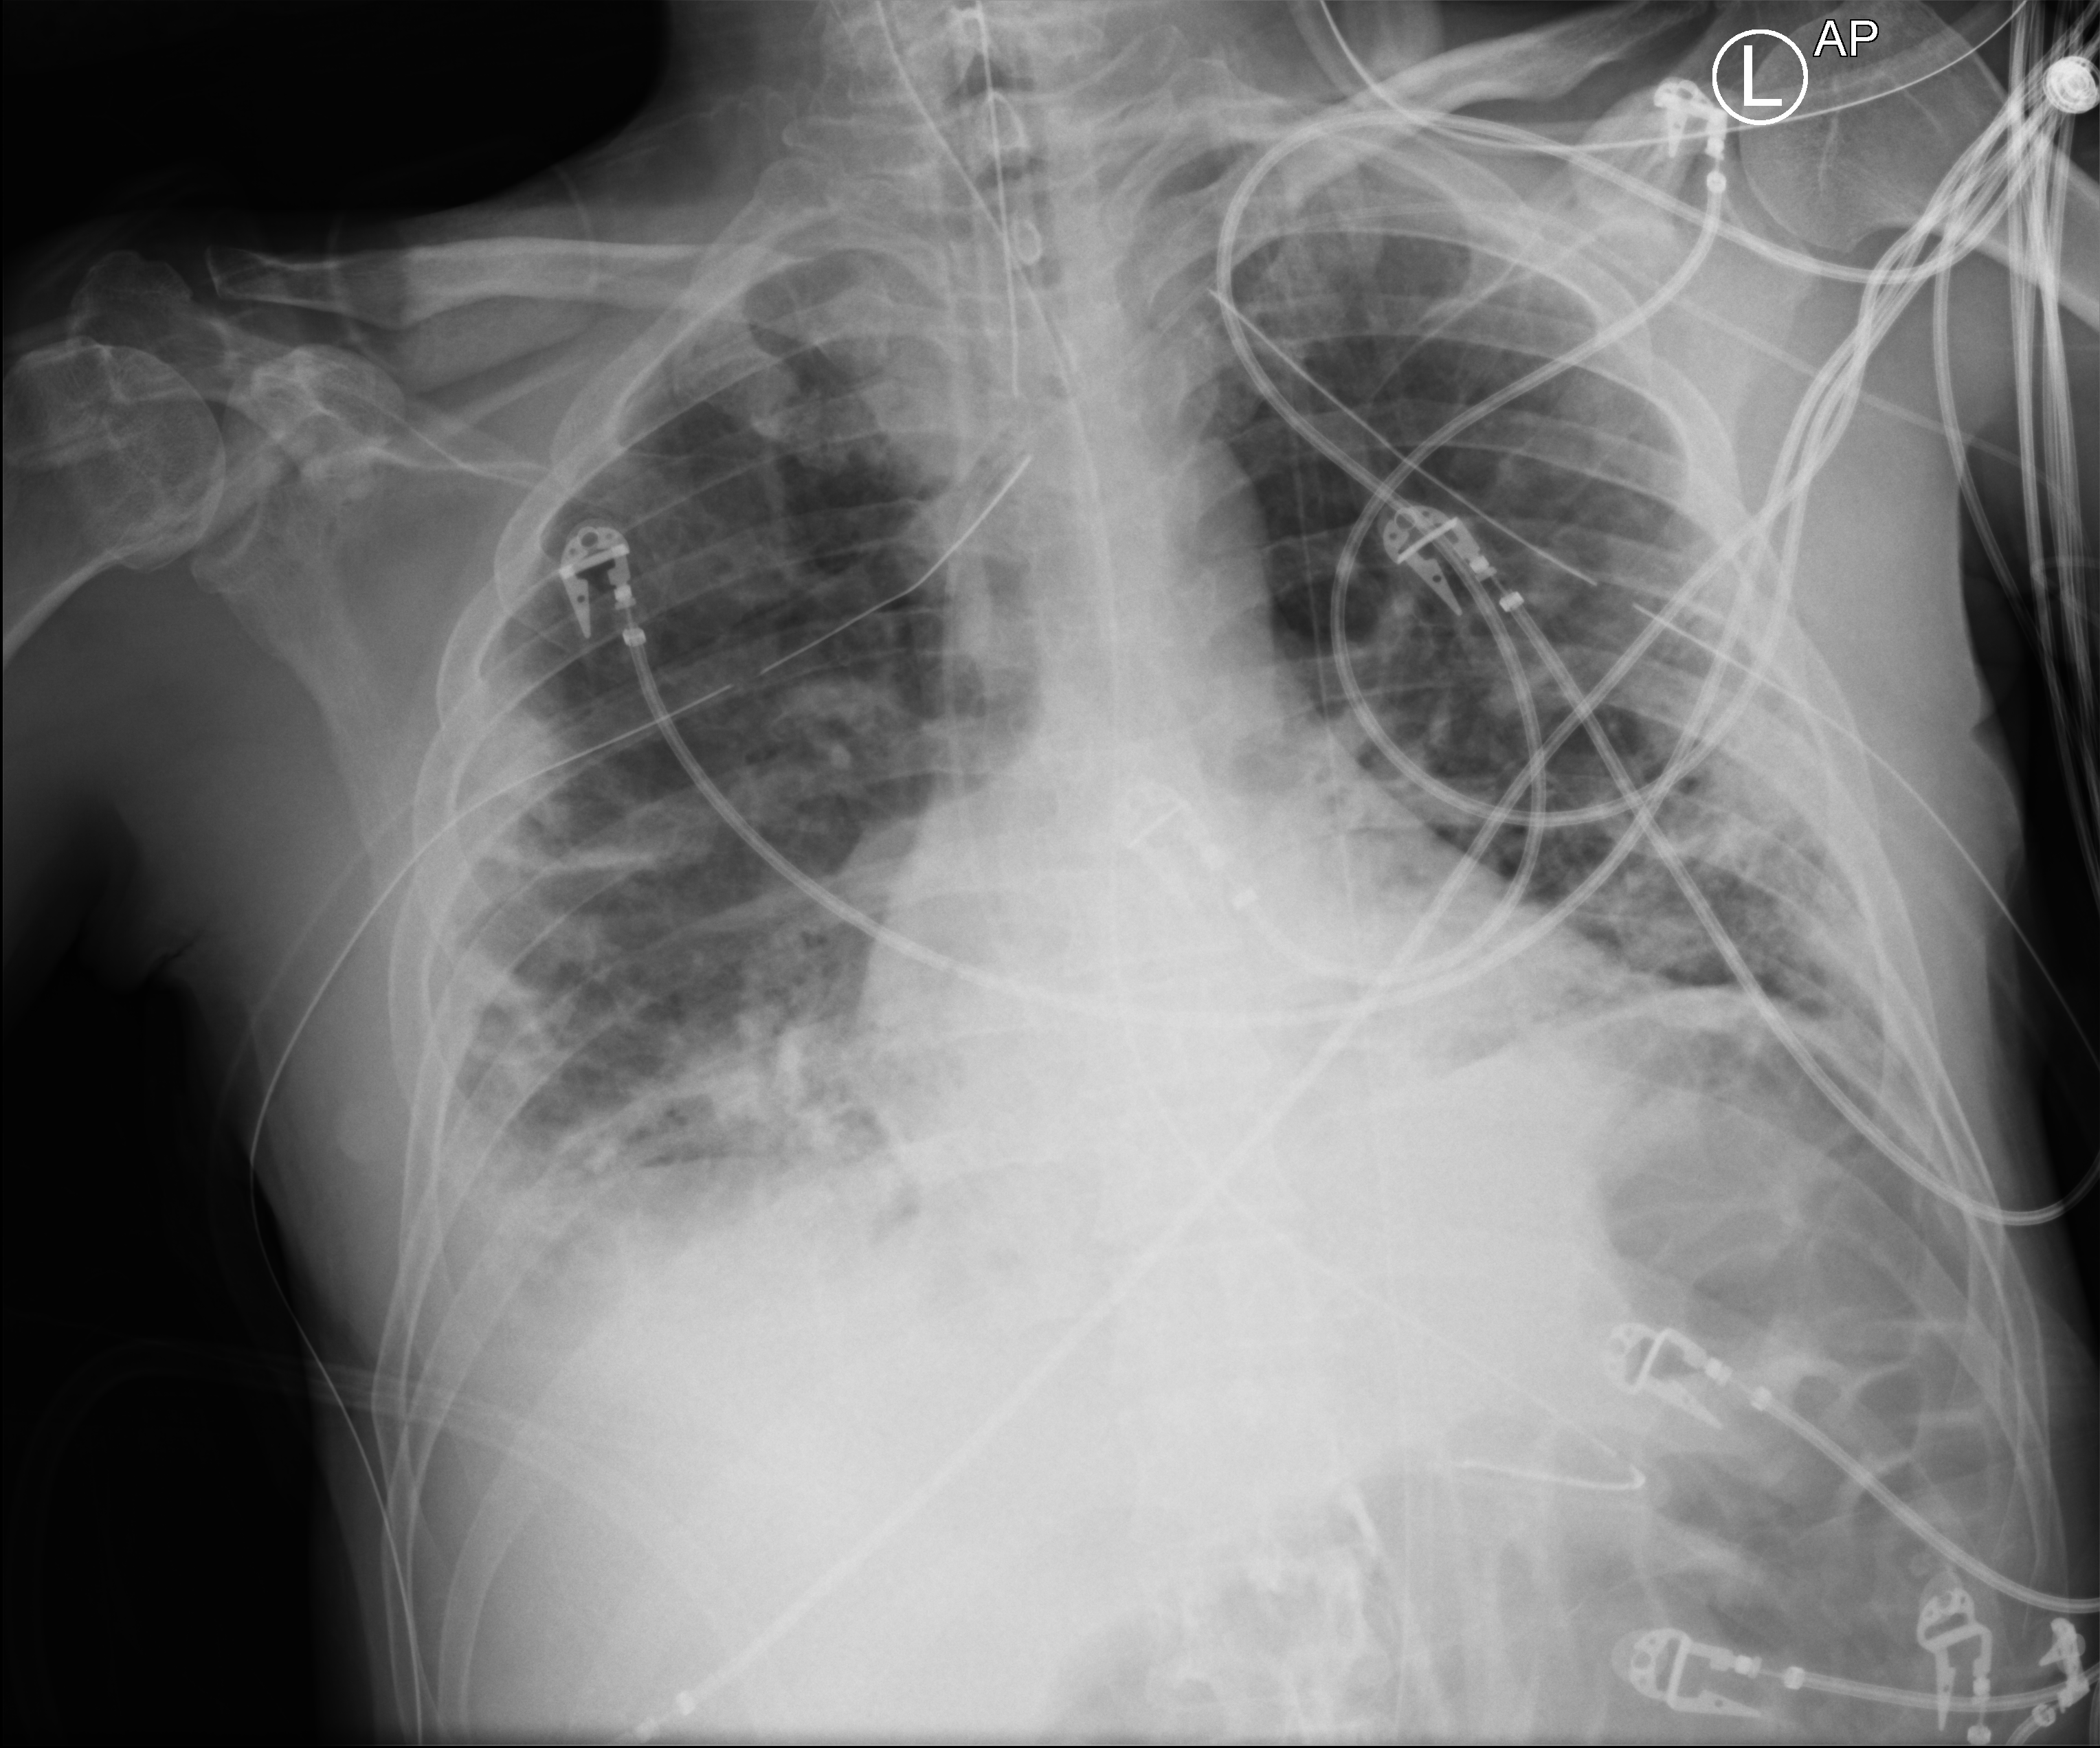
Portable chest radiograph. Patient hospitalised with COVID-19; male, aged 18–59 years.
From the hospital-stay record, not from the radiograph (when in the stay this image was taken is not recorded): mechanically ventilated during this hospital stay: yes.